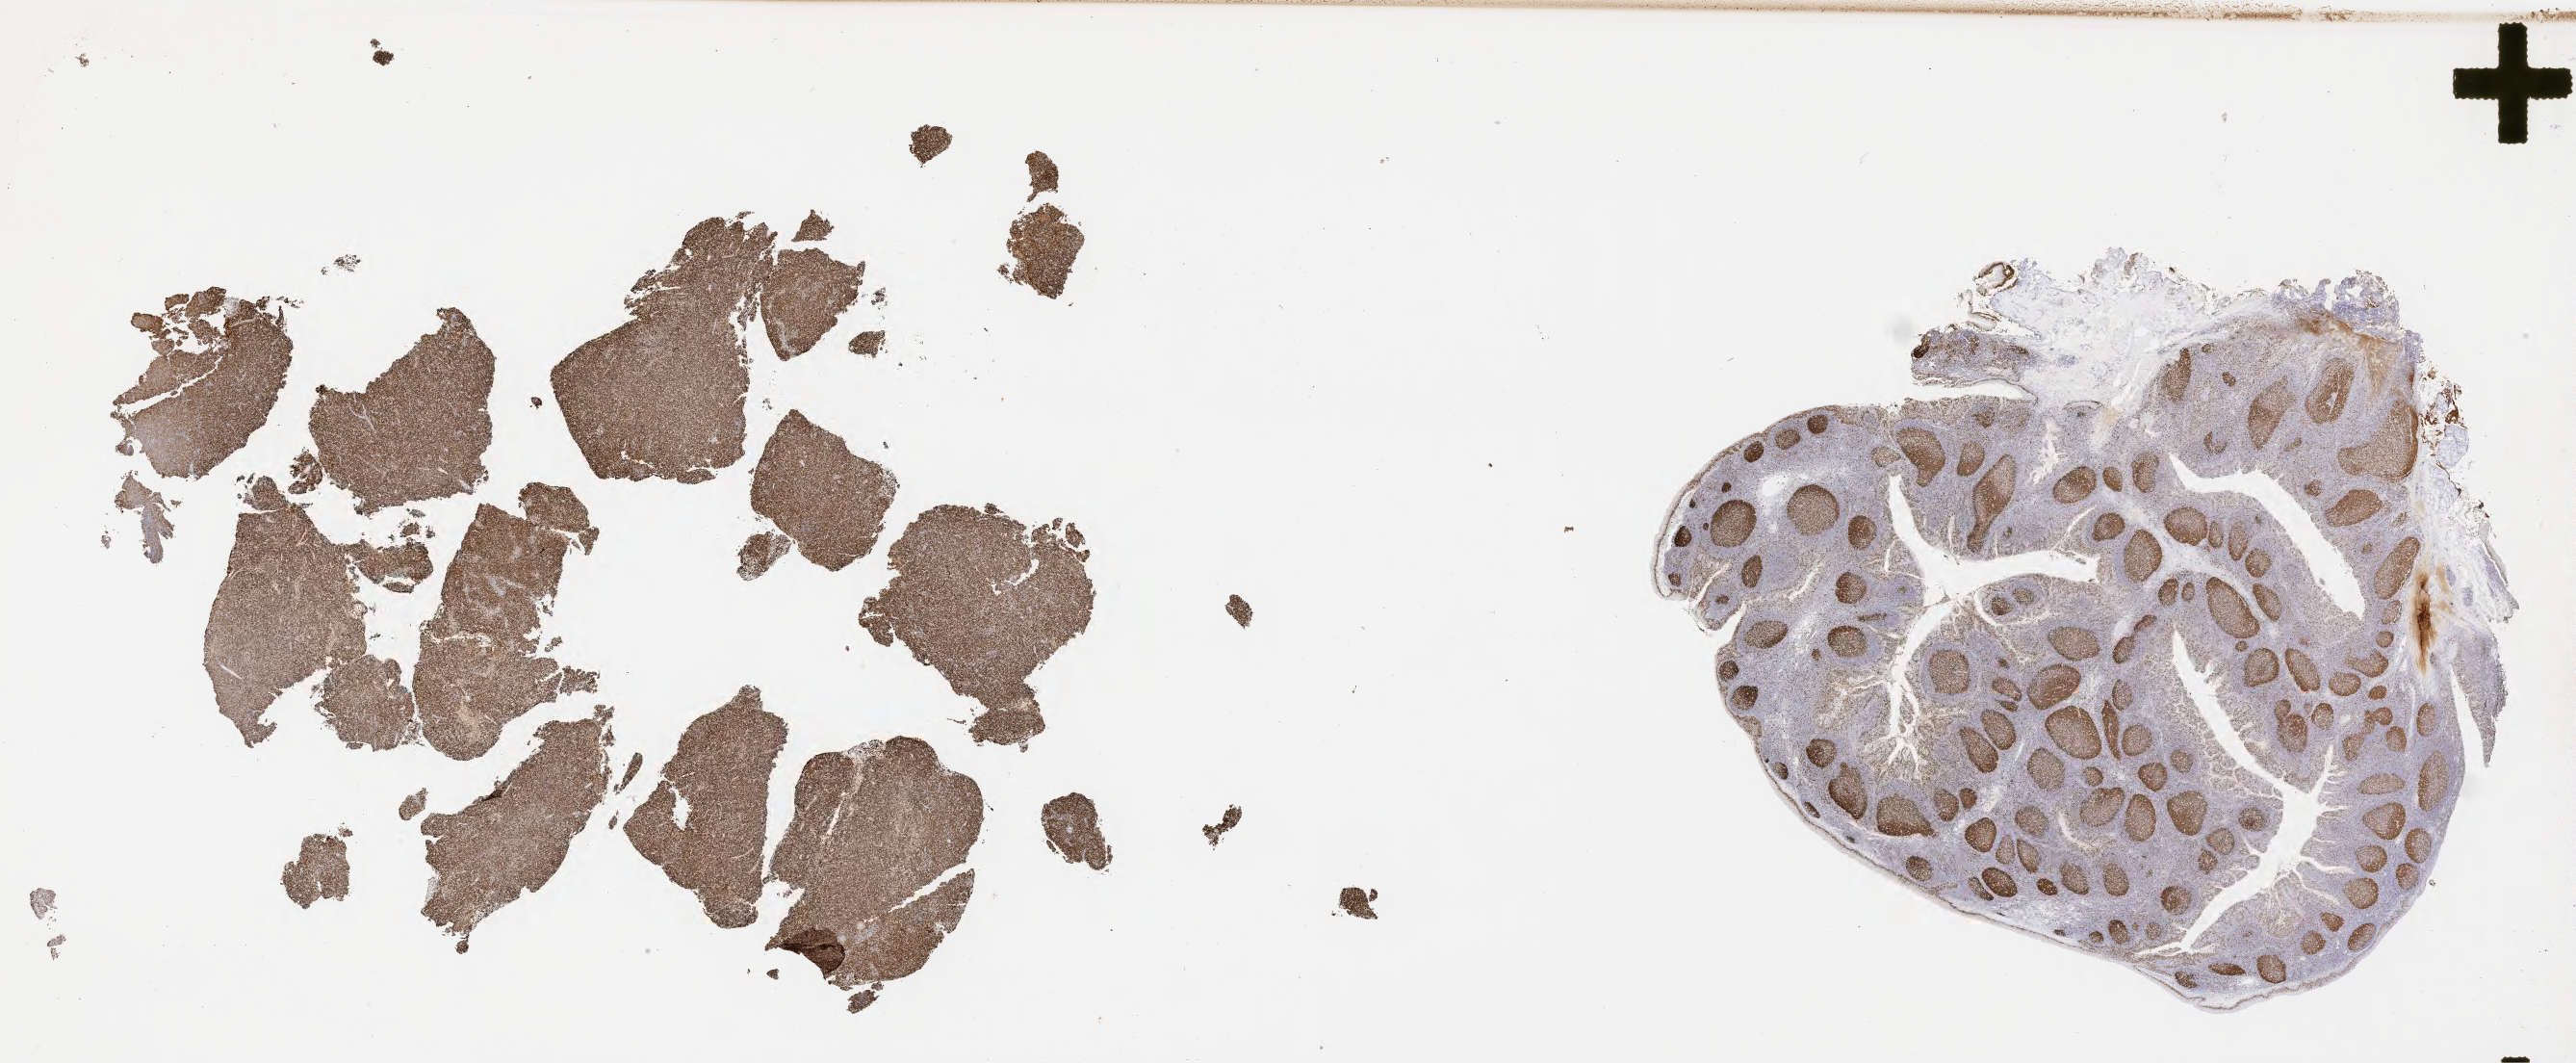
IHC for Ki-67, whole-slide image, shown as a low-resolution overview of the whole scanned area (about 43.3 x 17.8 mm), tumor tissue, anatomic site: lymph node. Patient female; aged 50.
Diagnosis: Diffuse large B-cell lymphoma, NOS.